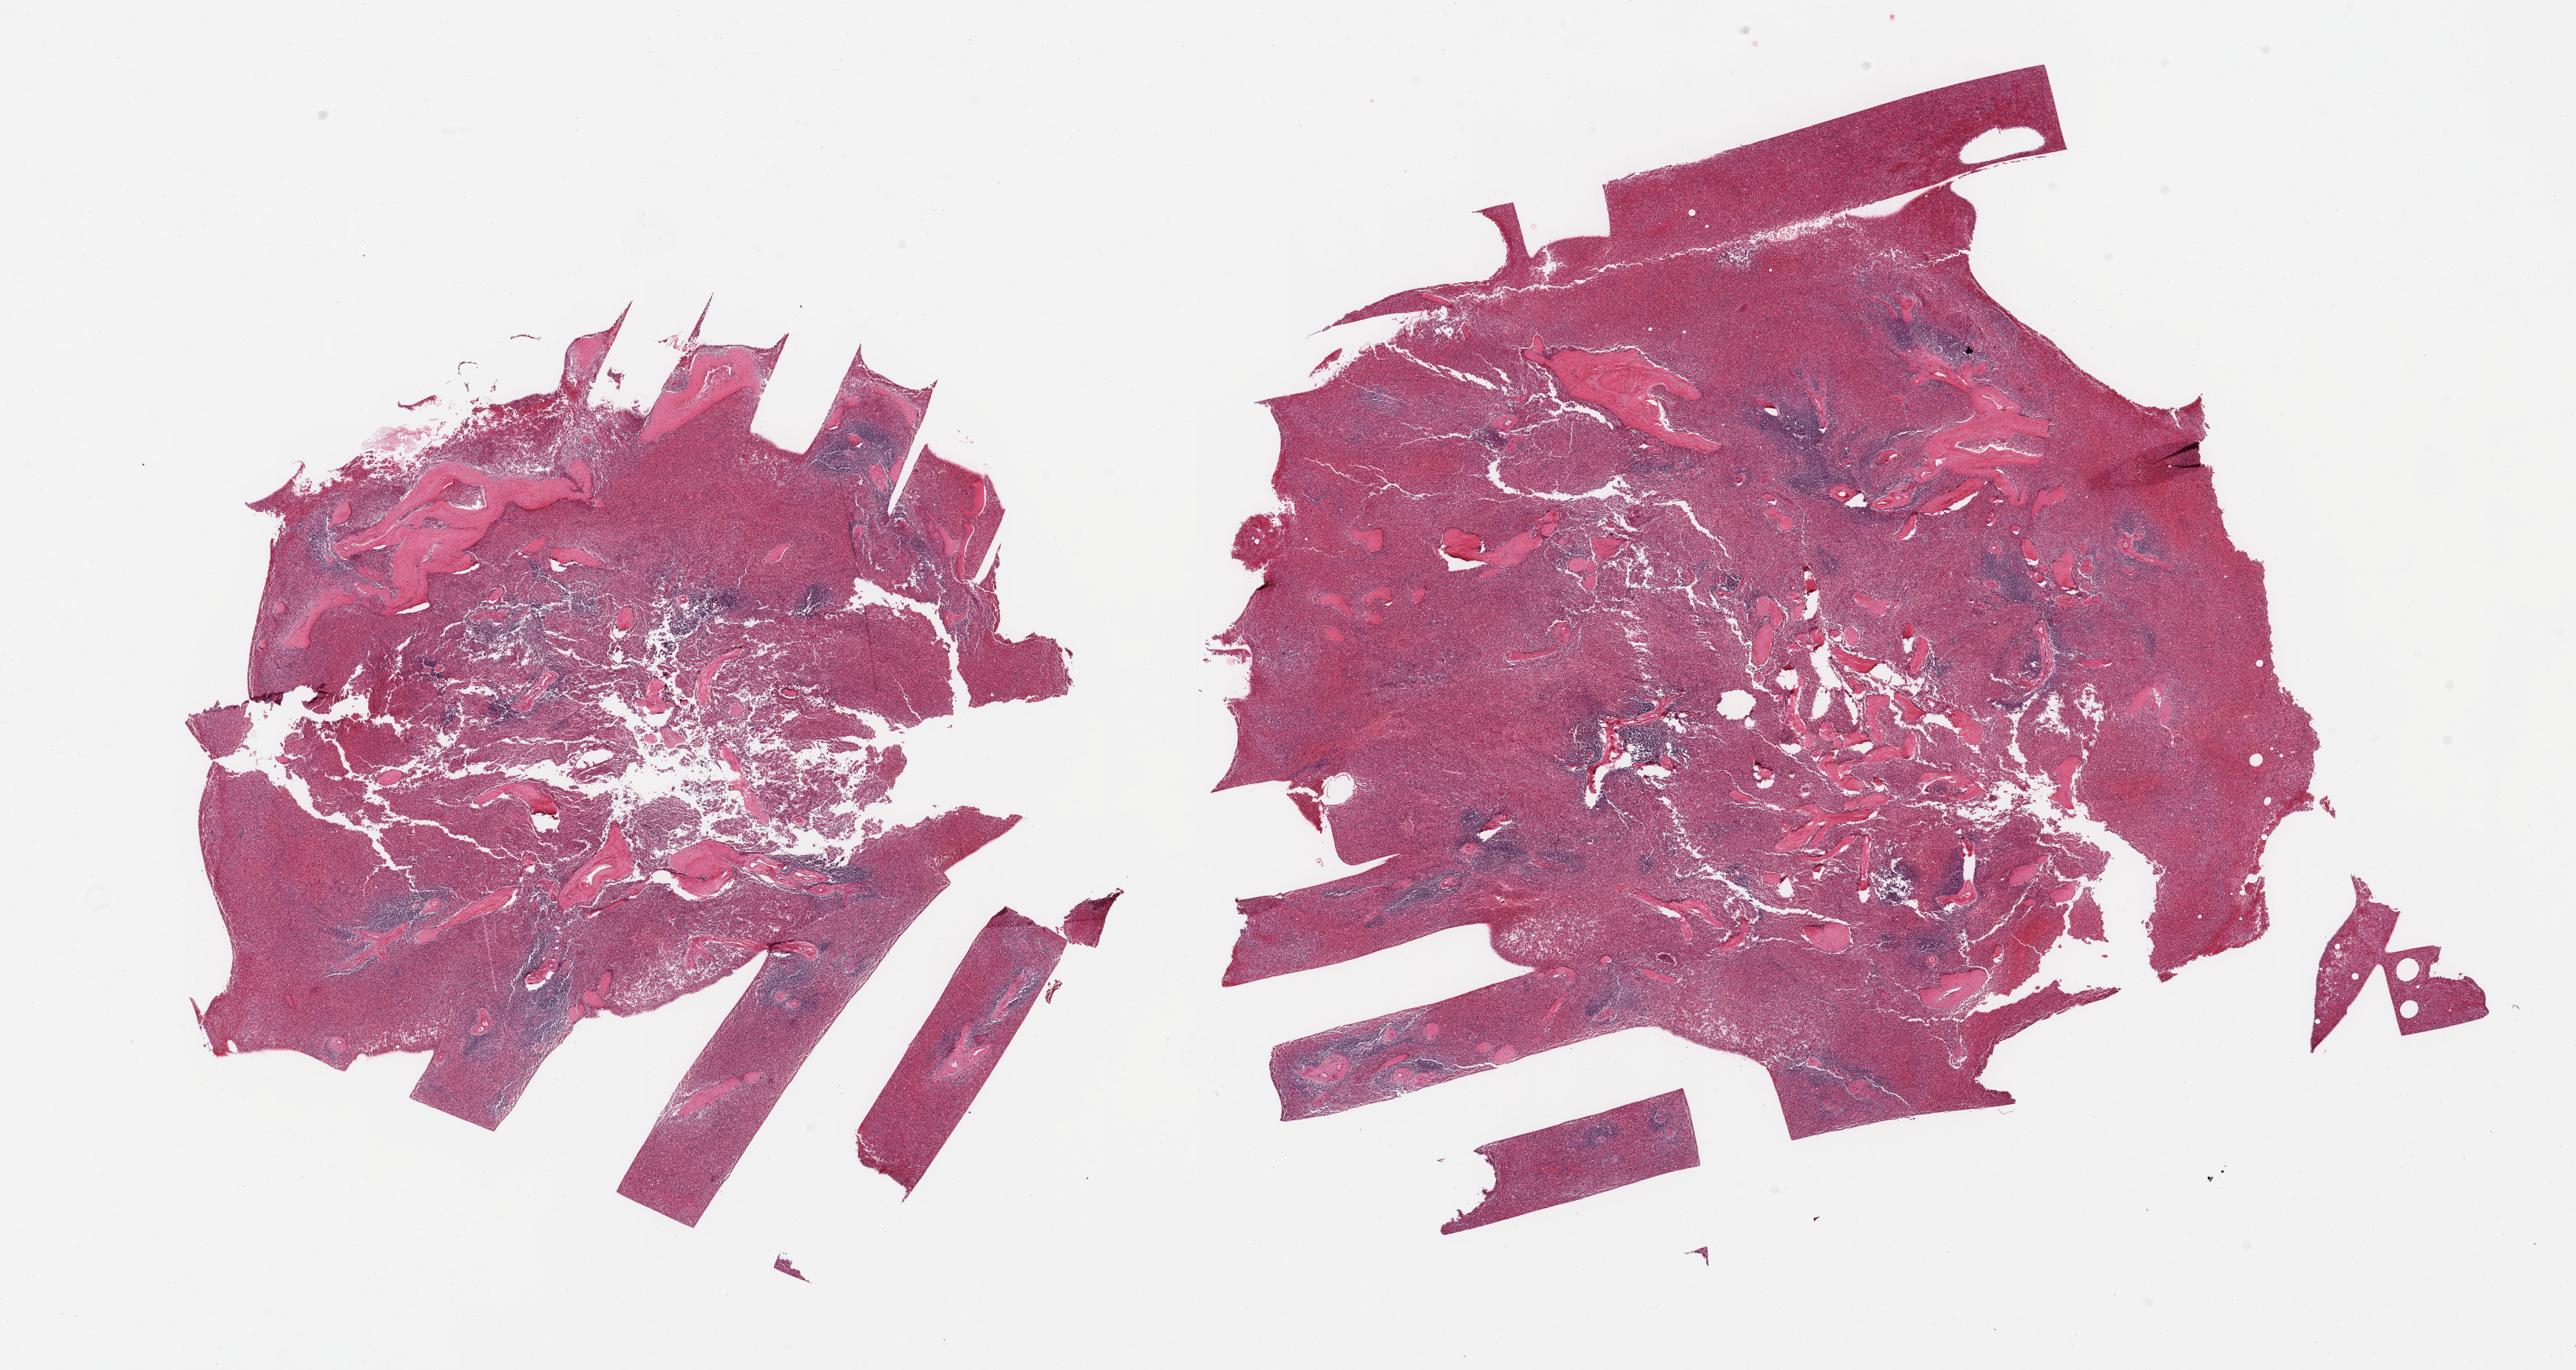
Digitized haematoxylin and eosin-stained section — whole scanned area (about 27.6 x 14.7 mm) shown as a low-resolution overview, PAXgene-fixed paraffin-embedded (PFPE) section, sampled site (target tissue): spleen, tissue donor sample. Donor sex: male.
Review note (as recorded): 2 pieces, moderate congestion.